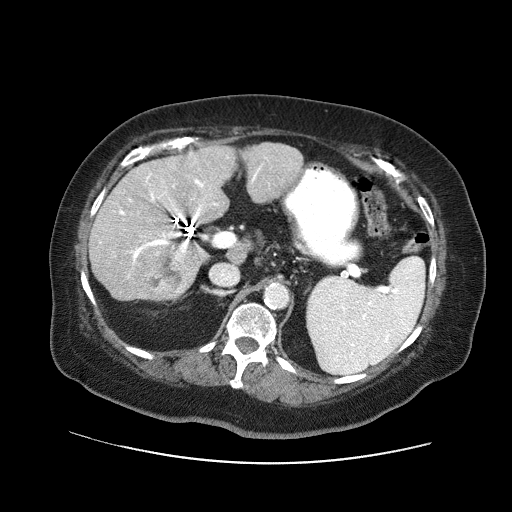
Contrast-enhanced abdominal CT (liver protocol), one axial slice; position 26 of 71 along the scan axis; 120 kVp; soft-tissue window (W 400 / L 40 HU); 2.5 mm slice thickness; 512 × 512 image matrix, field of view 400 × 400 mm. Case-level facts recorded for this patient, not image findings: diagnosis: hepatocellular carcinoma (patient treated with transarterial chemoembolisation; whether this scan precedes or follows treatment is not stated here); TNM stage (as recorded): Stage-II; Child-Pugh class: A.
Annotated regions visible in this slice (semi-automatic segmentation, software-assisted and operator-edited):
- liver parenchyma outside the tumour (the mass and vessels are separate outlines, so this box may not span the whole liver): box from (x=88, y=142) to (x=302, y=300) px
- mass: (x=146, y=253)–(x=185, y=292)
- liver vessels: (x=119, y=166)–(x=262, y=292)